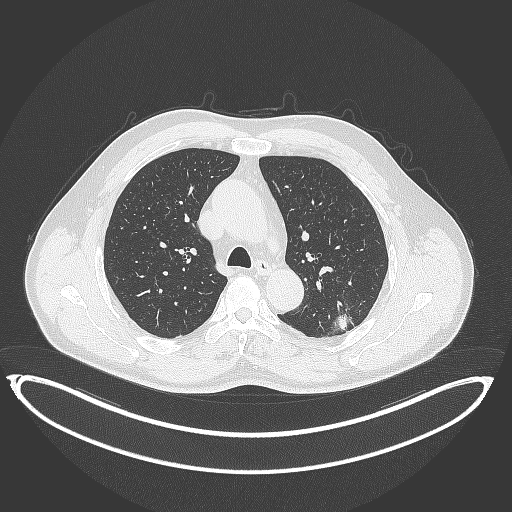
Chest CT, one axial slice; slice 247 of 399 in the series (ordered by position); reconstruction kernel B70f; 120 kVp; lung window (W 1500 / L -600 HU); 1 mm slice thickness; 512 × 512 image matrix, field of view 469 × 469 mm. Patient: male, 58 years. Case-level facts recorded for this patient, not image findings: clinical TNM (as recorded): T1c N0 M0.
Annotated regions visible in this slice (rectangle marked by the reading radiologist):
- lung tumour (recorded histology: adenocarcinoma): bounding box (x1, y1, x2, y2) in pixels: (323, 307, 355, 338)